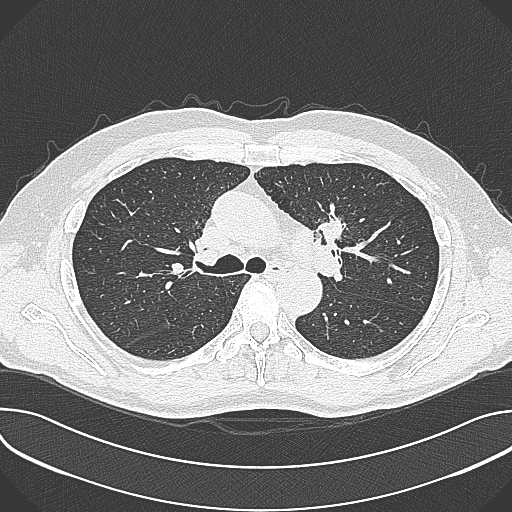
Low-dose screening chest CT, axial slice. Baseline annual screen. Lung window (W 1500 / L -600 HU). 120 kVp. 512 × 512 image matrix. Male participant, aged 59 years at enrolment. Current smoker at enrolment.
Expert-annotated lung lesion, box from (x=303, y=194) to (x=364, y=257) px. The screening reader recorded 2 non-calcified nodules or masses ≥4 mm on this exam (left upper lobe, left upper lobe); which of them this box marks is not recorded. Participant outcome: lung cancer diagnosed 21 days after this screen — non-small cell carcinoma, left upper lobe, poorly differentiated (G3), stage IIIA (AJCC 6th edition), 35 mm at pathology.